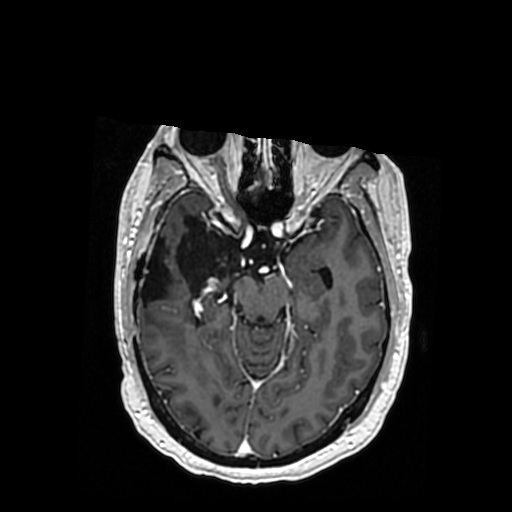
Brain MRI from a brain-tumour surgery series, one axial slice; position 217 of 364 along the scan axis; T1-weighted post-contrast; 512 × 512 image matrix, field of view 260 × 260 mm. From the clinical record (not read from this slice): histopathology: Oligodendroglioma; WHO grade: 3; IDH mutation: yes.
Annotated regions visible in this slice (expert manual segmentation):
- previous resection cavity: box from (x=140, y=217) to (x=240, y=306) px